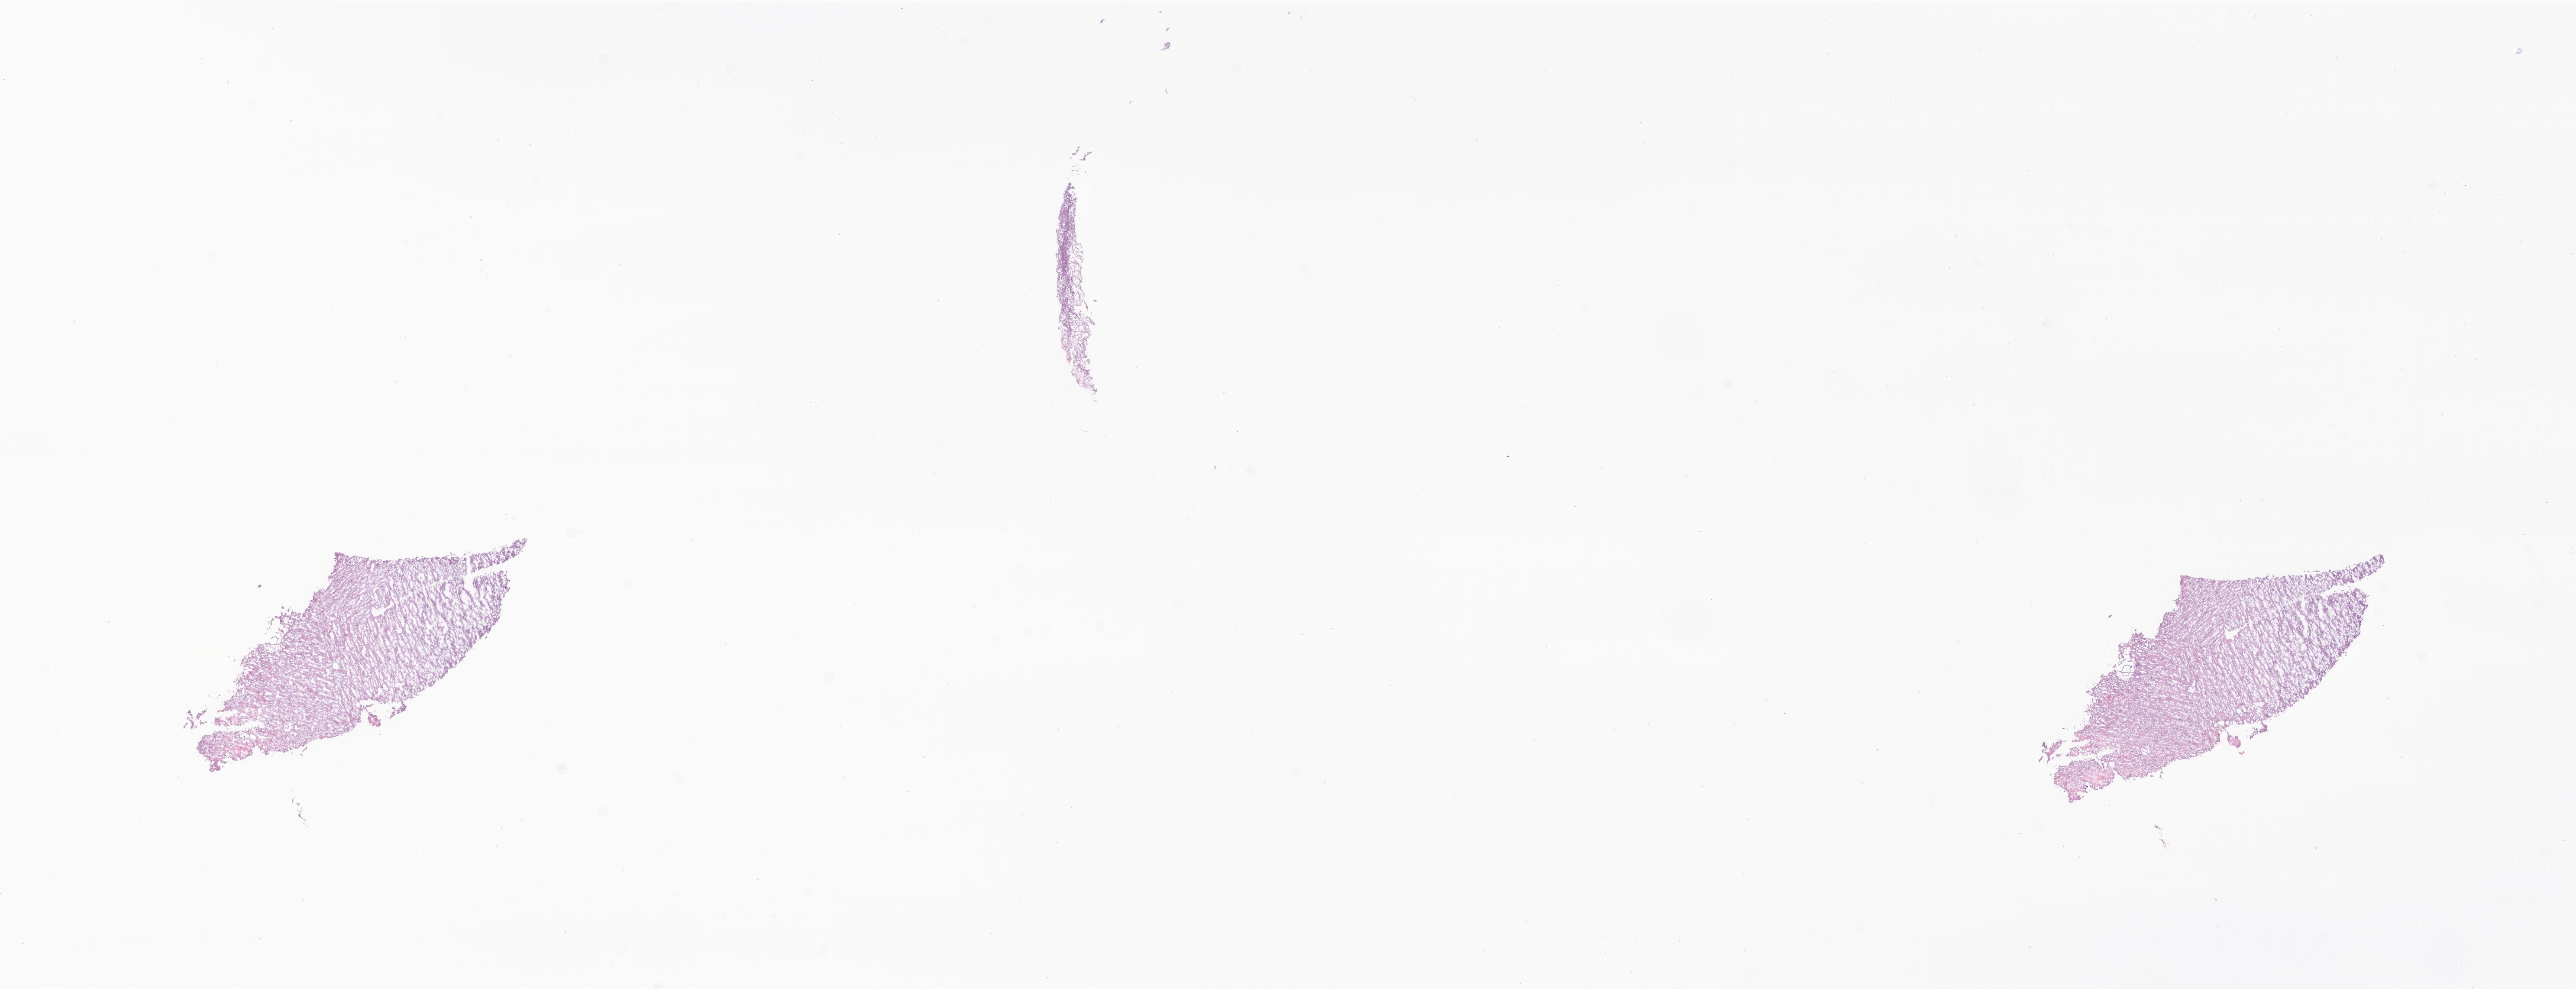
H&E whole-slide image of tumor tissue from the brain — shown as a low-resolution overview of the whole scanned area (about 25.1 x 9.6 mm); frozen section. Female patient, age 41 months (3 years 5 months).
* diagnosis (ICD-O-3 morphology term): Glioma, malignant